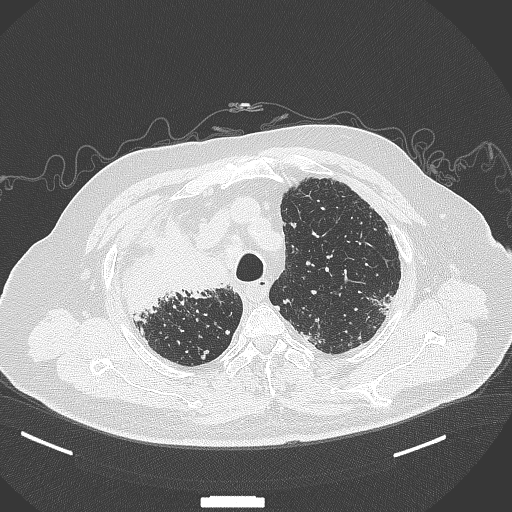
Chest CT, one axial slice. Slice 288 of 384 in the series (ordered by position). Lung window (W 1500 / L -600 HU). 1 mm slice thickness. 512 × 512 image matrix. Patient: male, 69 years. Case-level facts recorded for this patient, not image findings: clinical TNM (as recorded): T4 N3 M1.
Annotated regions visible in this slice (rectangle marked by the reading radiologist):
- lung tumour (recorded histology: adenocarcinoma): bounding box (x1, y1, x2, y2) in pixels: (121, 213, 234, 323)